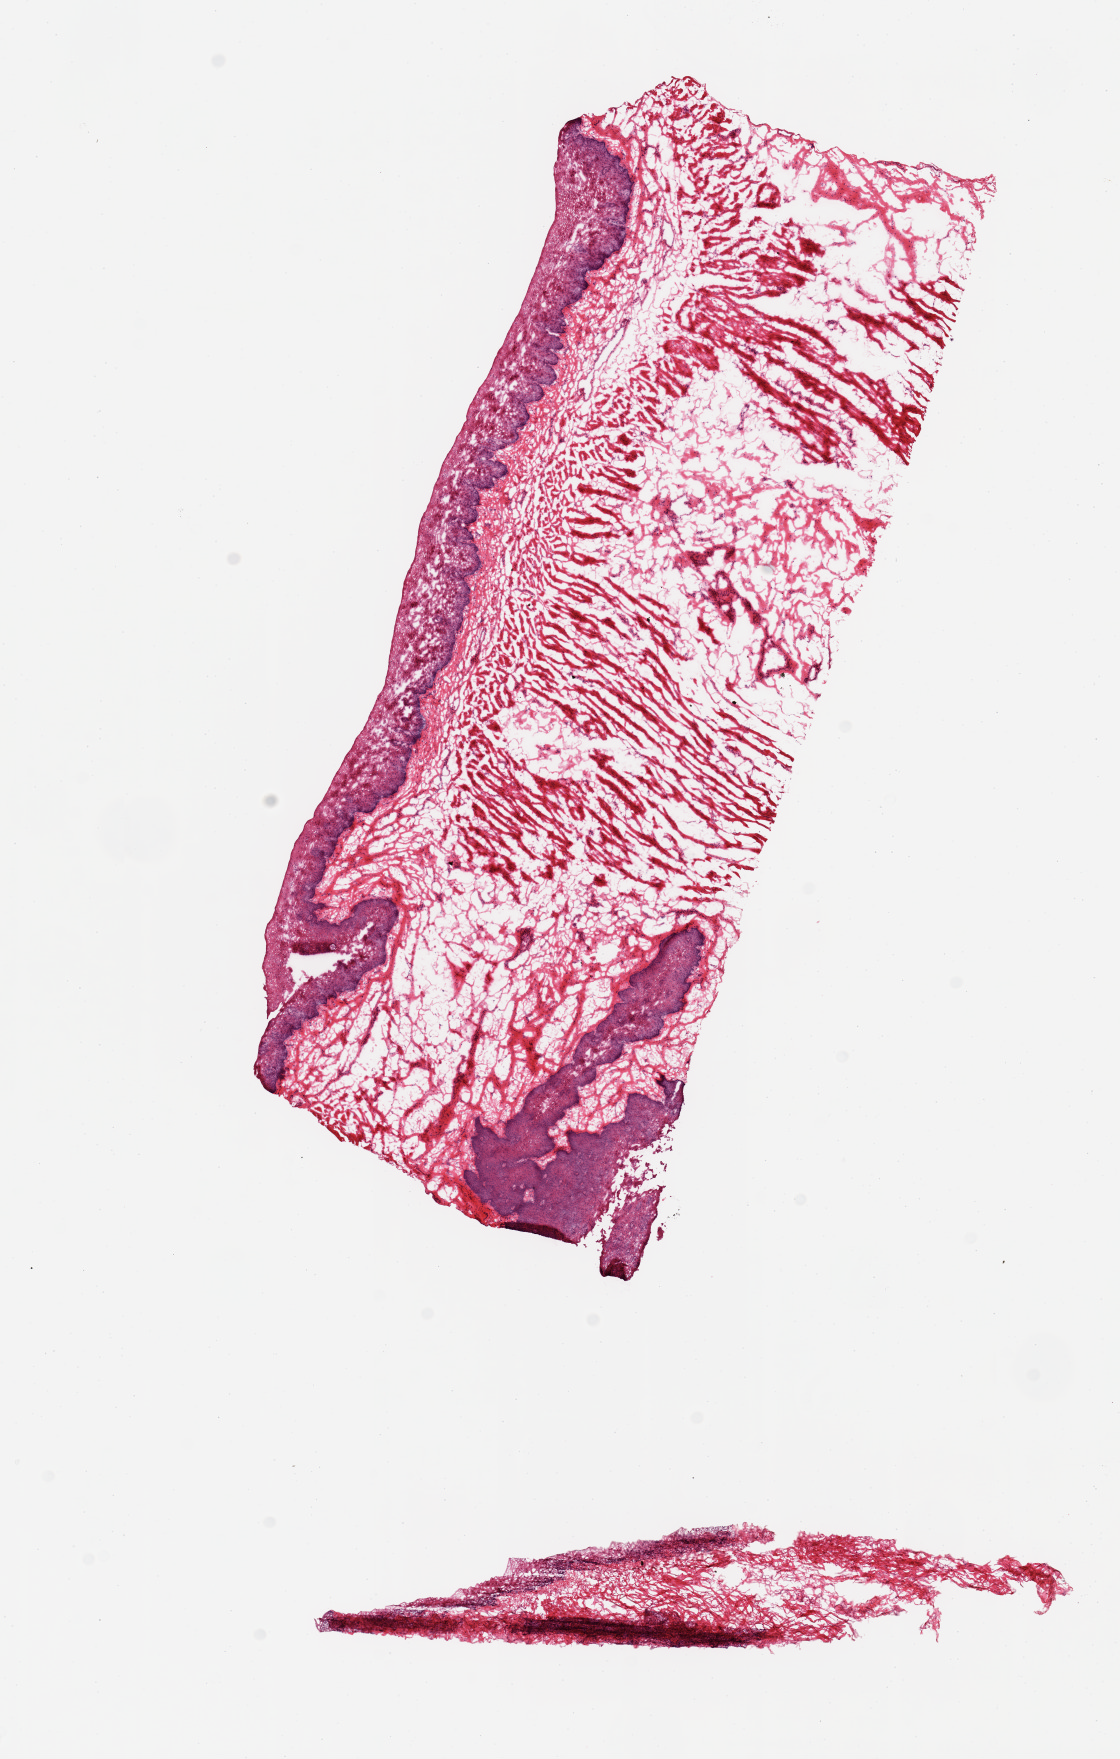
Hematoxylin and eosin (H&E) whole-slide image — whole scanned area (about 8.9 x 13.9 mm, slide scanned at 20x) shown as a low-resolution overview, frozen section (dry ice), target tissue: esophageal mucous membrane, donor tissue sample.
Pathologist's review note for this sample: 2 pieces.